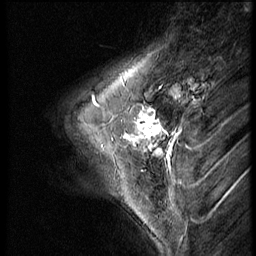
Breast MRI (dynamic contrast-enhanced), one sagittal slice. Slice 16 of 56 in the series (ordered by position). Dynamic contrast-enhanced series, image 2 of 3 at this slice position (ordered by acquisition). 1.5 T. TE 4.2 ms, TR 9 ms. 2.5 mm slice thickness. 256 × 256 image matrix, field of view 180 × 180 mm. Female patient, age 46 years. From the clinical record (not read from this slice): setting: breast cancer imaged before/during neoadjuvant chemotherapy; receptor status: HER2-positive.
Annotated regions visible in this slice (semi-automatically segmented with operator editing):
- analysis volume of interest (the breast-tissue region the enhancement analysis was run in; not a lesion): bounding box [x1, y1, x2, y2] px = [64, 98, 174, 182]
- tumour enhancement mask (voxels above the 140 % enhancement threshold inside the analysis volume of interest): [126, 107, 164, 154]